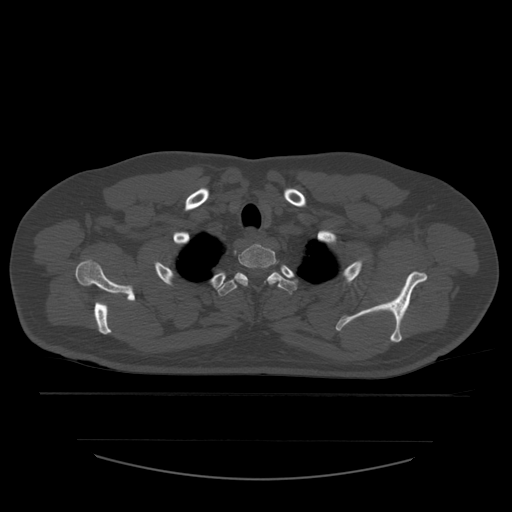
CT including the spine, one axial slice. Position 459 of 532 along the scan axis. 120 kVp. Bone window (W 1800 / L 400 HU). 1.25 mm slice thickness. 512 × 512 image matrix. Patient age 44 years. Case-level facts recorded for this patient, not image findings: primary cancer: soft tissue sarcoma.
Outlined on this slice (semi-automatically segmented with operator editing):
- T1 vertebra: bounding box (x1, y1, x2, y2) in pixels: (237, 244, 279, 286)
- T2 vertebra: (218, 272, 297, 296)
- T3 vertebra: (288, 280, 291, 282)